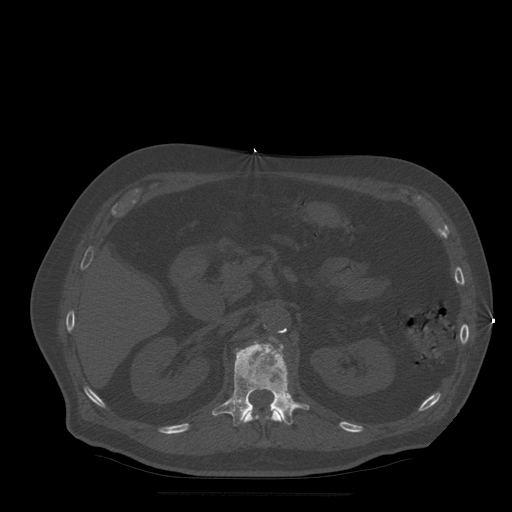
CT including the spine, one axial slice. Slice 201 of 522 in the series (ordered by position). Bone window (W 1800 / L 400 HU). 1.25 mm slice thickness. 512 × 512 image matrix, field of view 420 × 420 mm. Patient age 72 years. Case-level facts recorded for this patient, not image findings: primary cancer: prostate.
Outlined on this slice (semi-automatically segmented with operator editing):
- L1 vertebra: bounding box [x1, y1, x2, y2] px = [212, 337, 310, 427]
- T12 vertebra: [243, 409, 282, 424]